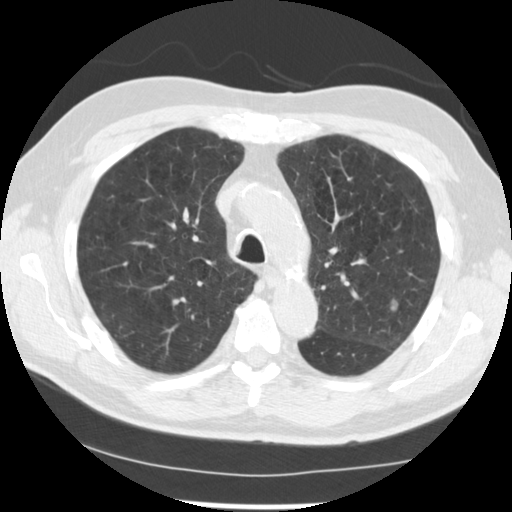
Low-dose screening chest CT, one axial slice; slice 178 of 249 in the series (ordered by position); lung window (W 1500 / L -600 HU); 2.5 mm slice thickness; 512 × 512 image matrix, field of view 341 × 341 mm.
Outlined on this slice (outlined manually by an expert reader):
- lesion 1 (tumor, upper lobe of left lung): bounding box [x1, y1, x2, y2] px = [390, 298, 399, 311]